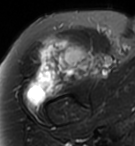
MRI of an extremity soft-tissue mass, one axial slice; position 76 of 95 along the scan axis; T2-weighted fat-saturated; MR volume resampled by the dataset authors to the PET/CT grid (not the native acquisition matrix); 135 × 146 image matrix, field of view 132 × 143 mm. Female patient. Case-level facts recorded for this patient, not image findings: histological type: pleiomorphic undifferentiated sarcoma; grade: high; site of the primary tumour: right quadricep.
Structures marked on this image (expert contour drawn on MRI and transferred to this co-registered scan by the dataset authors):
- gross tumour volume including surrounding oedema: bounding box (x1, y1, x2, y2) in pixels: (26, 36, 95, 105)
- gross tumour volume (mass): (26, 36, 95, 105)